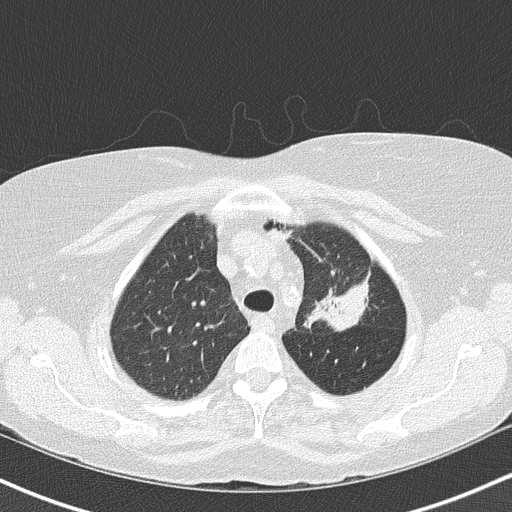
Low-dose screening chest CT, one axial slice. Position 121 of 147 along the scan axis. Reconstruction kernel B50f. Lung window (W 1500 / L -600 HU). 512 × 512 image matrix.
Annotated regions visible in this slice (outlined manually by an expert reader):
- lesion 1 (tumor, upper lobe of left lung): box from (x=315, y=281) to (x=368, y=330) px